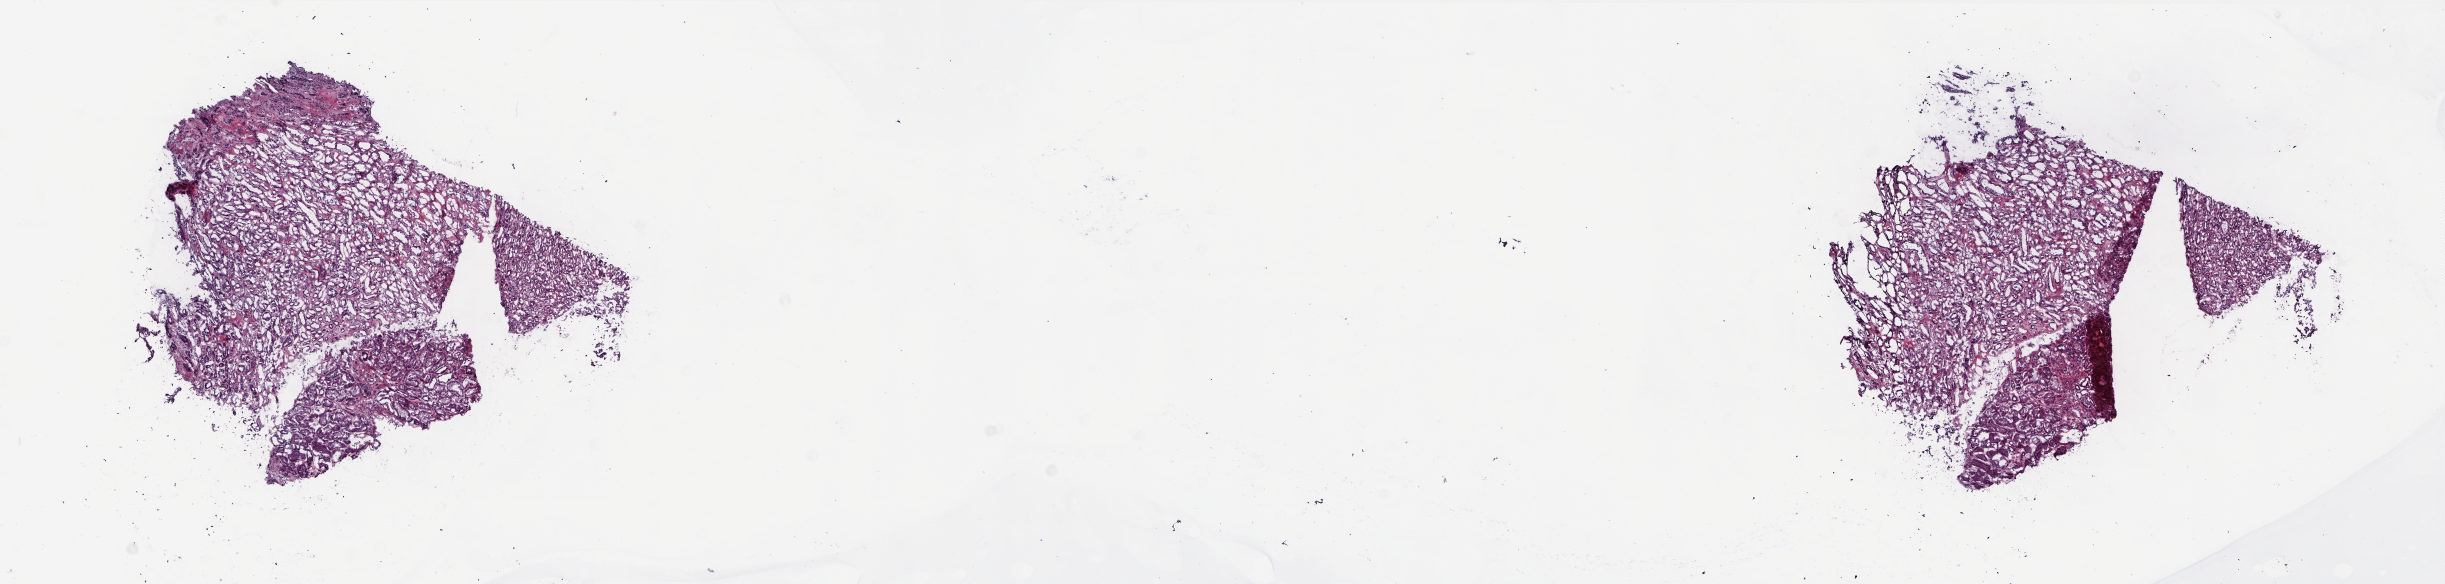
Whole-slide histology image, Hematoxylin and eosin (H&E) stained, whole scanned area (about 19.7 x 4.7 mm, from a 20x scan) shown as a low-resolution overview. Frozen section from the top of the tissue portion. Sample: solid tissue normal (non-tumour tissue), kidney. Male patient; age at initial diagnosis 57 years. Pathologist review of this section (percent, as recorded): tumour cells 0%, tumour nuclei 0%, normal cells 80%, stromal cells 20%, necrosis 0%. Inflammatory infiltration, as recorded: lymphocyte infiltration 0%, monocyte infiltration 0%, neutrophil infiltration 0%.
* this section: solid tissue normal (non-tumour) sample from the same patient
* patient diagnosis: Papillary adenocarcinoma, NOS